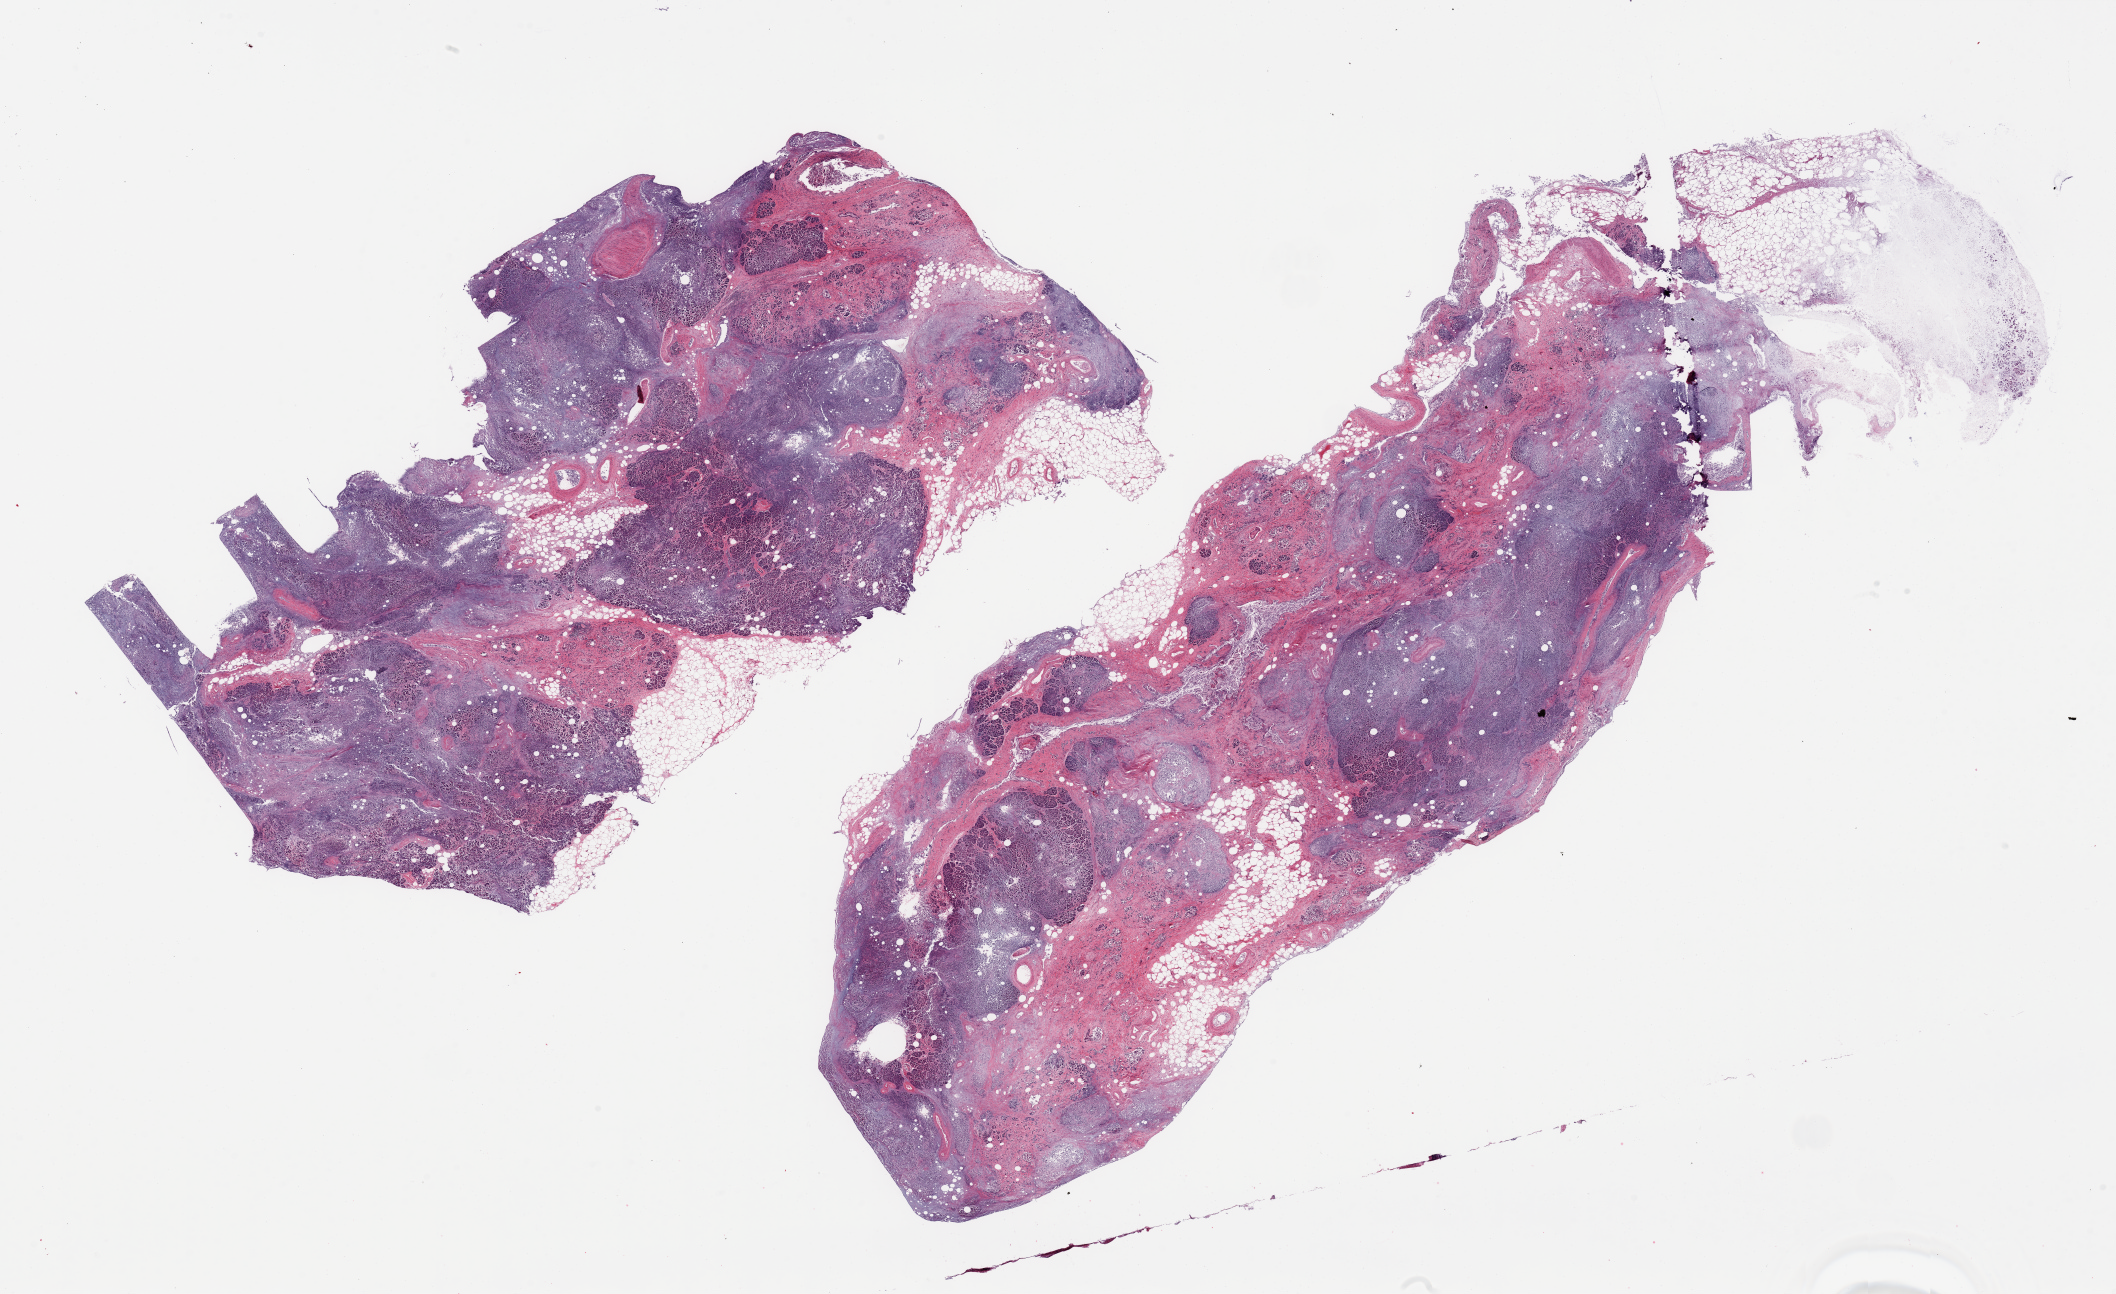
Haematoxylin and eosin whole-slide image — low-resolution overview of the scanned area, about 33.5 x 20.5 mm, PAXgene-fixed, paraffin-embedded tissue, target tissue: pancreas, tissue donor sample. Male donor.
Reviewer comment on this tissue sample: 2 pieces, advanced autolysis, Islets not visible.